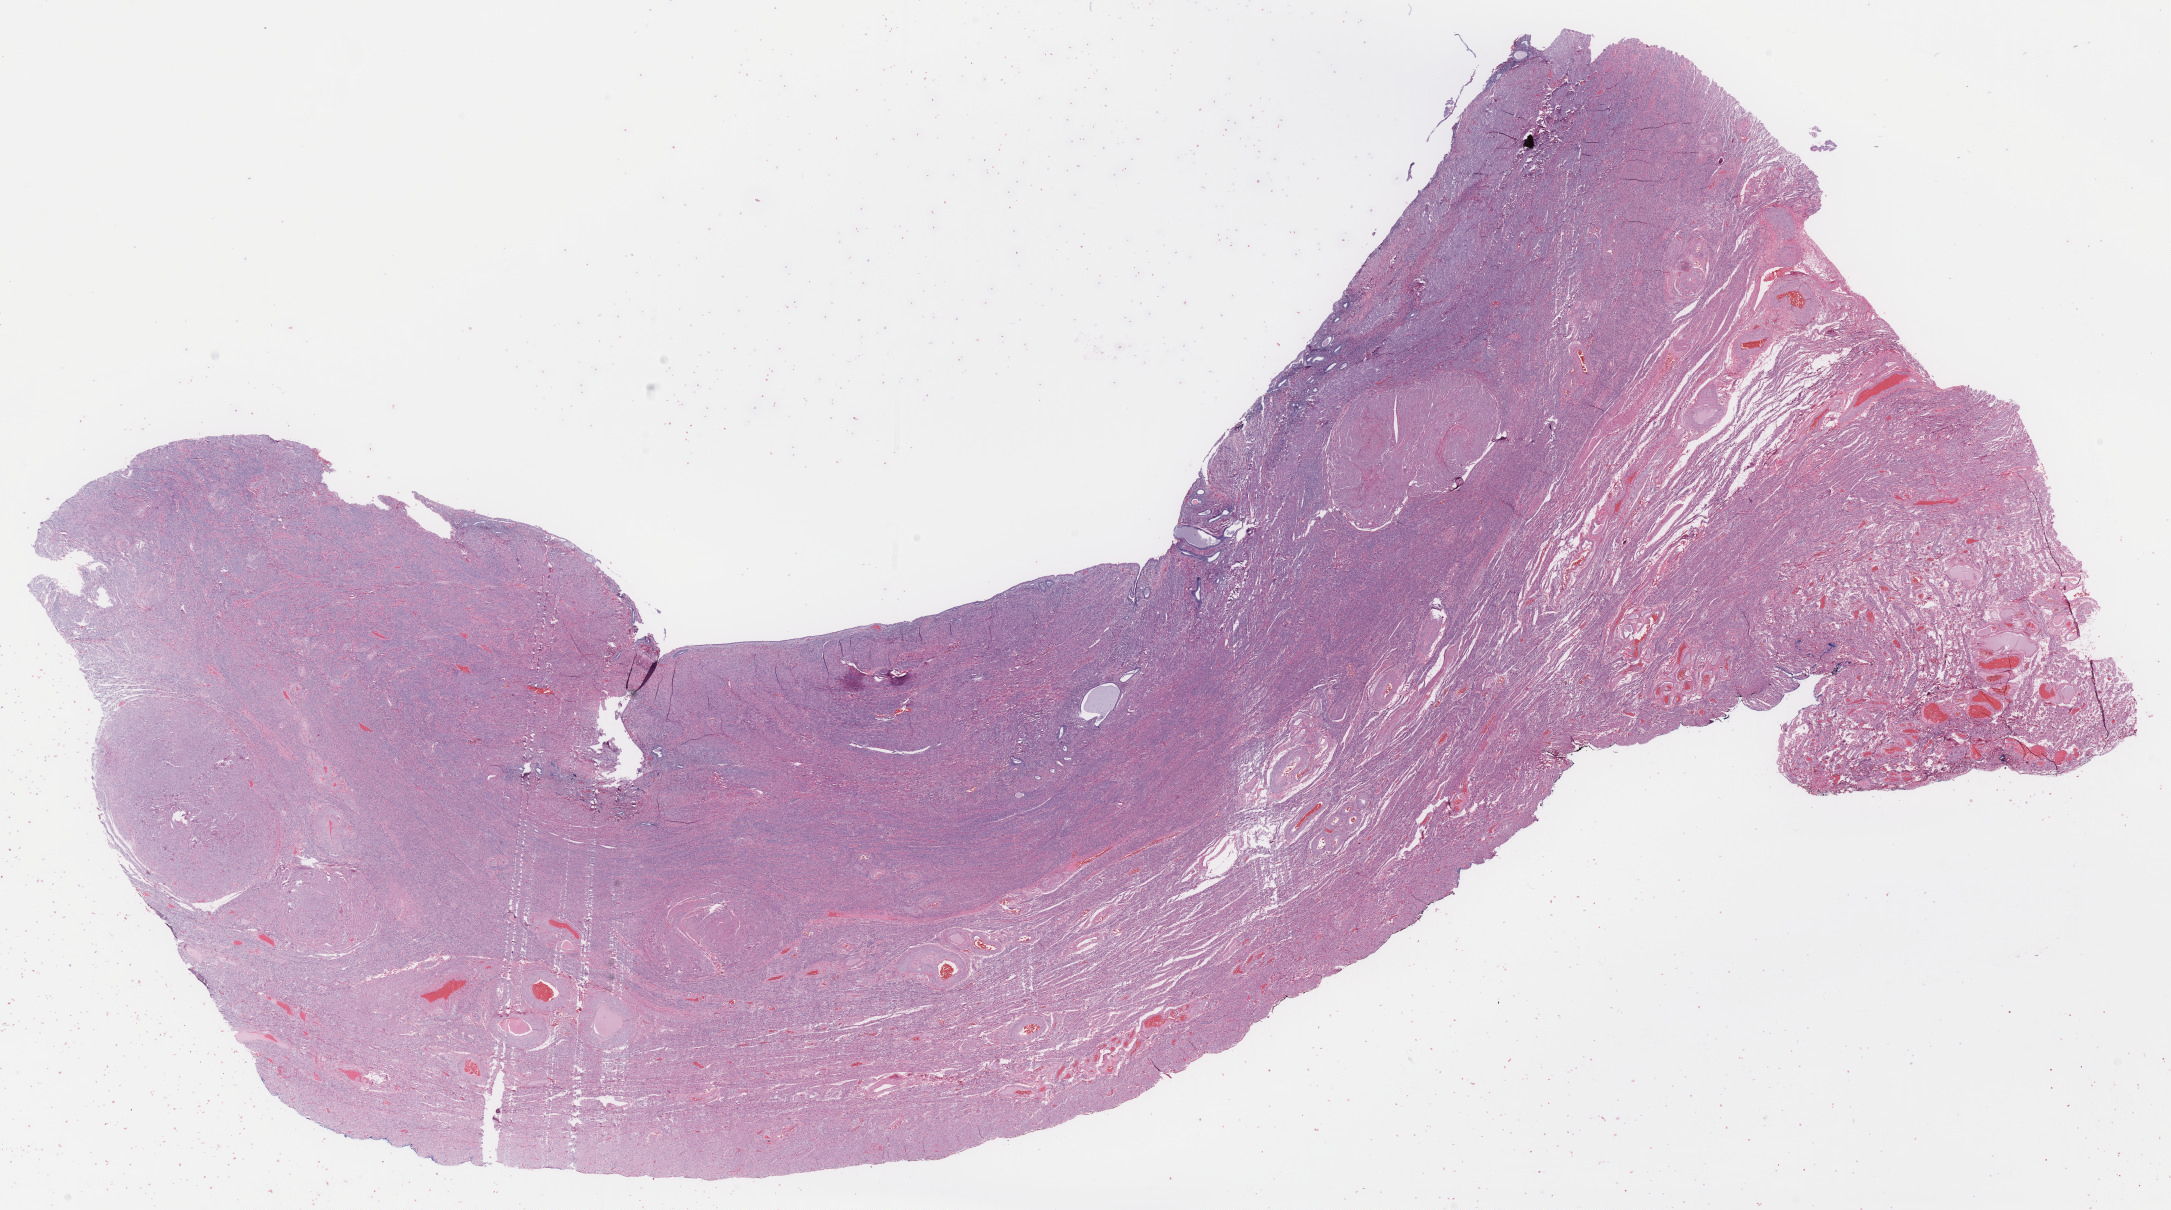
Haematoxylin and eosin whole-slide image — shown as a low-resolution overview of the whole scanned area (about 34.4 x 19.2 mm). Frozen section. Normal-tissue sample (non-tumor) from a patient with serous carcinoma, NOS. Anatomic site: body of uterus. Female patient. Composition of this section per pathologist review: tumor cells 1%, tumor nuclei 1%, stromal cells 0%, necrosis 0%, normal cells 99%. Infiltration values recorded for this section: lymphocyte infiltration 0%, monocyte infiltration 0%, neutrophil infiltration 0%.
* this section: non-tumor tissue sample; the patient's diagnosis is given above